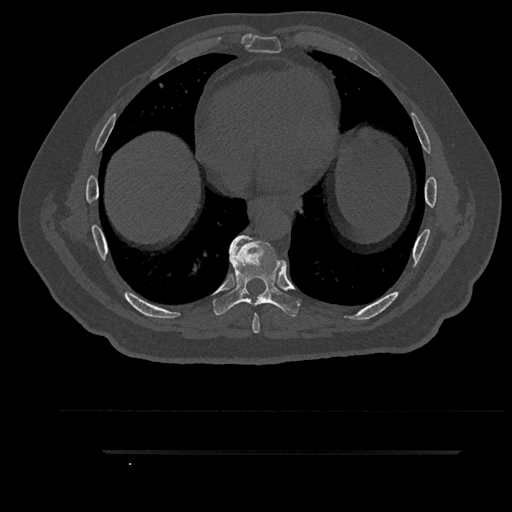
CT including the spine, one axial slice. Position 489 of 797 along the scan axis. Reconstruction kernel Br40s/3. 120 kVp. Bone window (W 1800 / L 400 HU). 0.5 mm slice thickness. 512 × 512 image matrix, field of view 432 × 432 mm. Patient: male, 63 years. From the clinical record (not read from this slice): primary cancer: renal; vertebrae with lytic lesions (as recorded): T8.
Structures marked on this image (semi-automatically segmented with operator editing):
- T7 vertebra: box from (x=237, y=241) to (x=260, y=334) px
- T8 vertebra: (x=213, y=235)–(x=299, y=316)